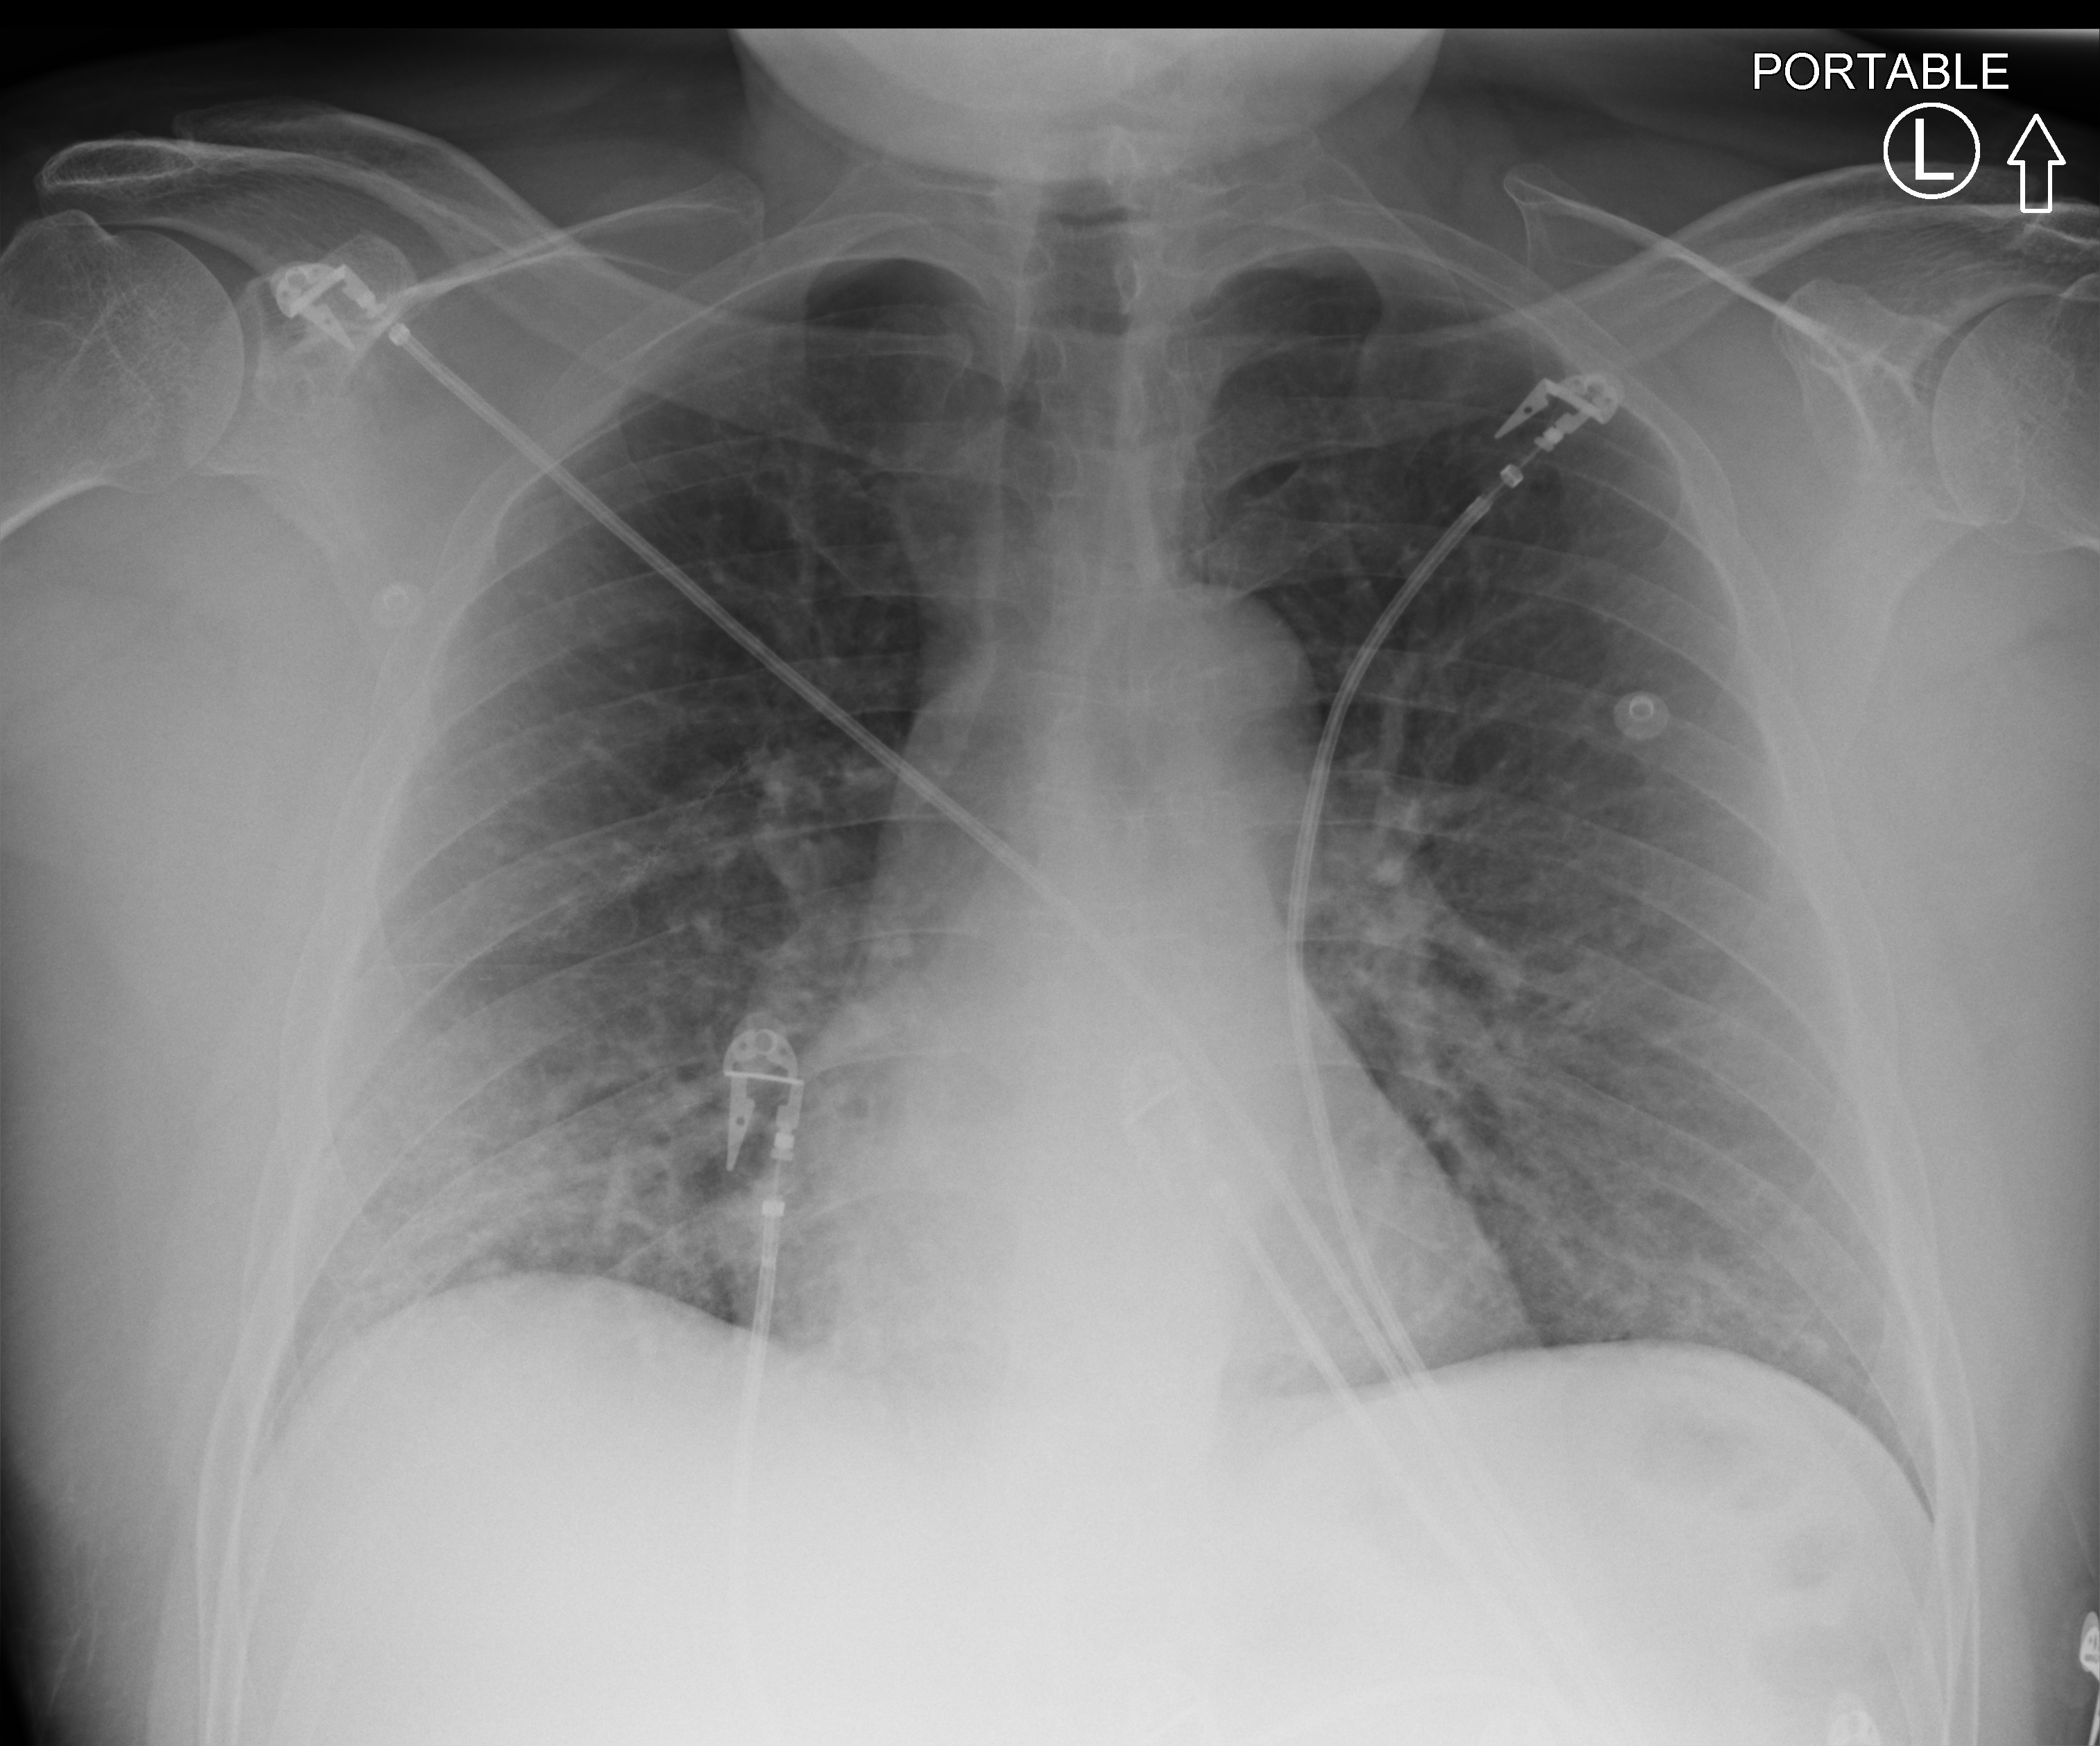
Chest X-ray (portable), anteroposterior (AP) projection. Male patient hospitalised with COVID-19, age 18–59 years.
Admission-level facts for this patient (not findings on this image; timing relative to this image not recorded): length of hospital stay: 13 days.